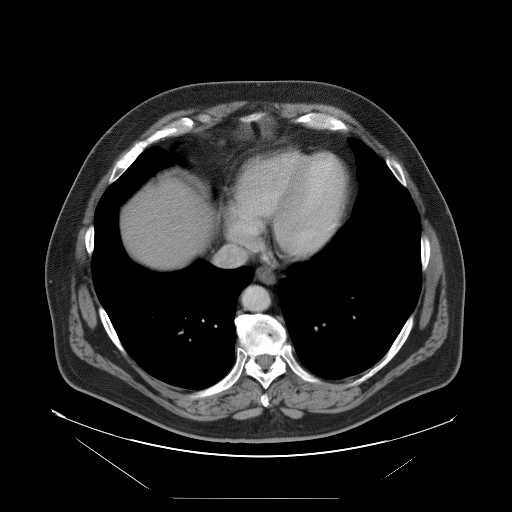
Contrast-enhanced abdominal CT, one axial slice. Position 95 of 114 along the scan axis. Intravenous contrast given. Soft-tissue window (W 400 / L 40 HU). 512 × 512 image matrix. Male patient, age 61 years. Case-level facts recorded for this patient, not image findings: diagnosis: colorectal cancer liver metastases, imaged before liver resection; multiple liver metastases: no; largest metastasis: 6.5 cm.
Annotated regions visible in this slice (outlined manually by an expert reader):
- hepatic veins: bounding box [x1, y1, x2, y2] px = [216, 214, 267, 266]
- liver: [123, 179, 208, 269]
- planned liver remnant (the part of the liver to remain after resection): [165, 179, 210, 240]